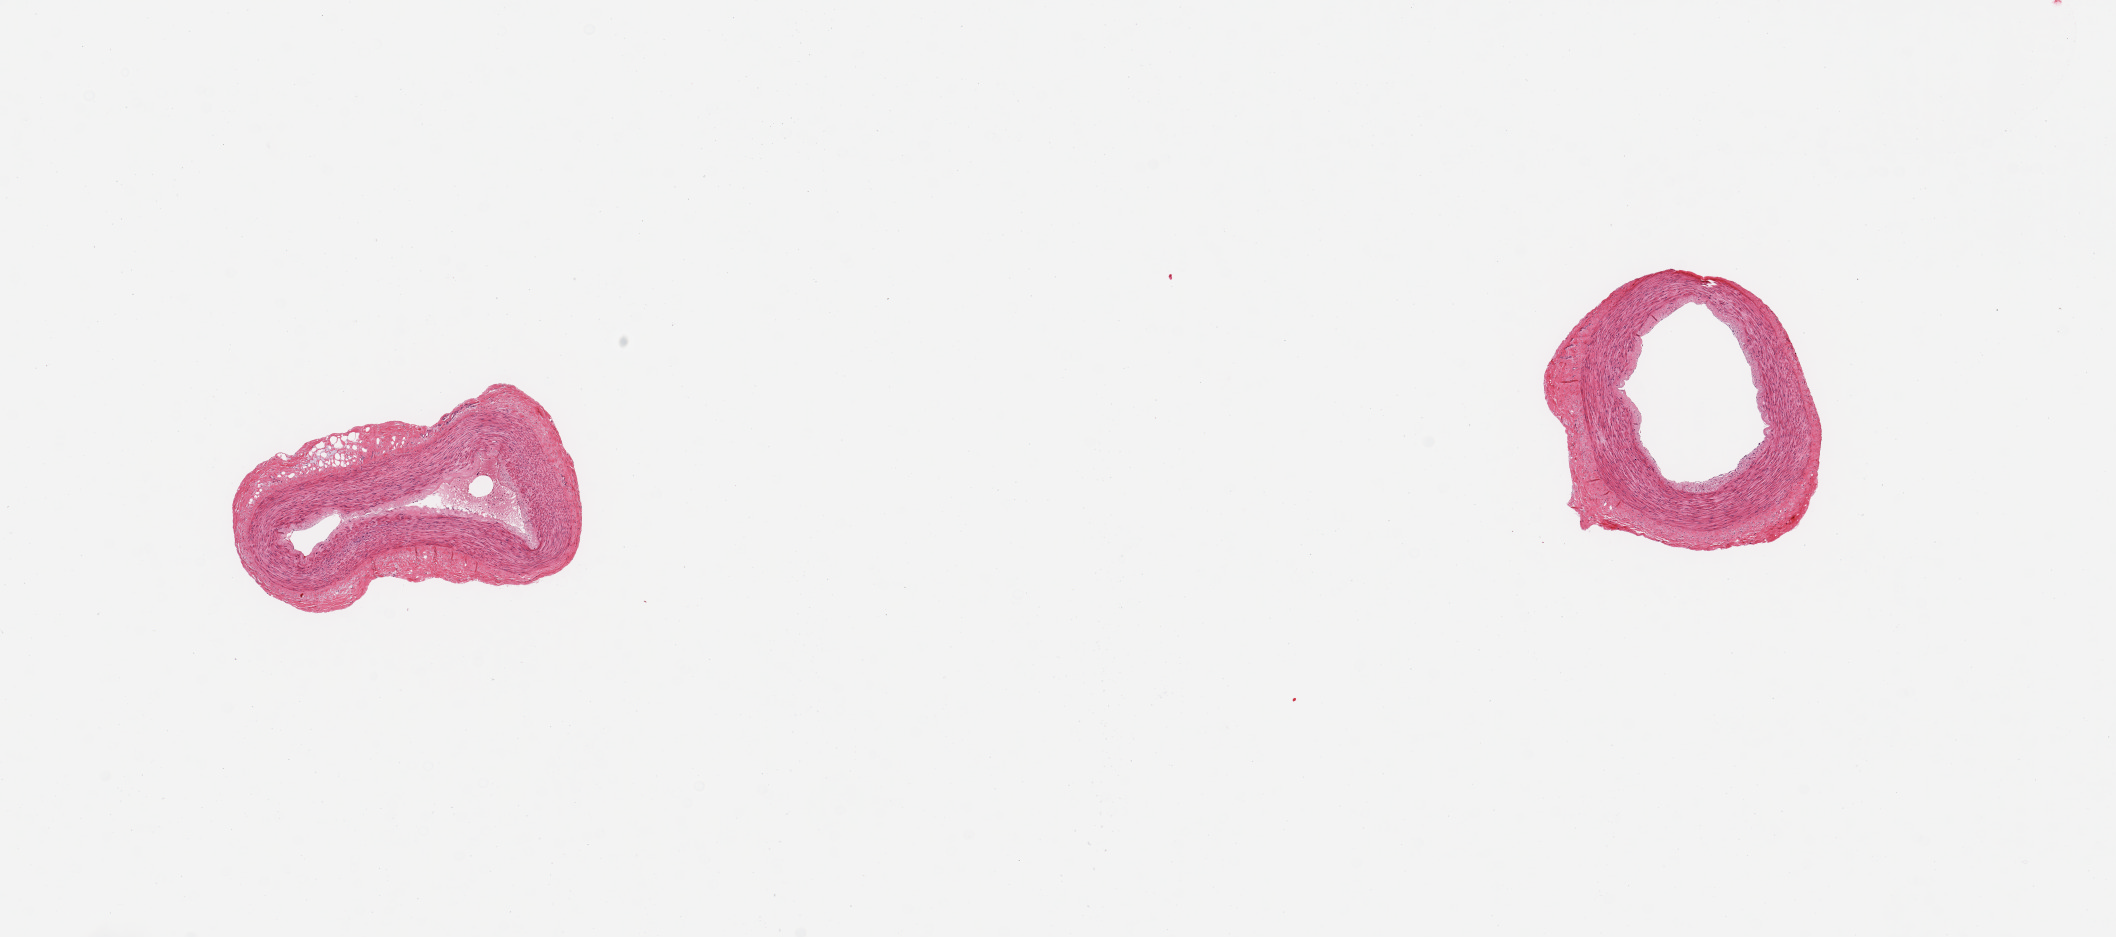
Digitized haematoxylin and eosin-stained section, shown as a low-resolution overview of the whole scanned area (about 16.7 x 7.4 mm, acquisition: 20x scan); PAXgene-fixed, paraffin-embedded tissue; sampled site (target tissue): tibial artery; tissue donor sample. Donor: male.
Reviewer comment on this tissue sample: 2 pieces, no significant adherent fat.